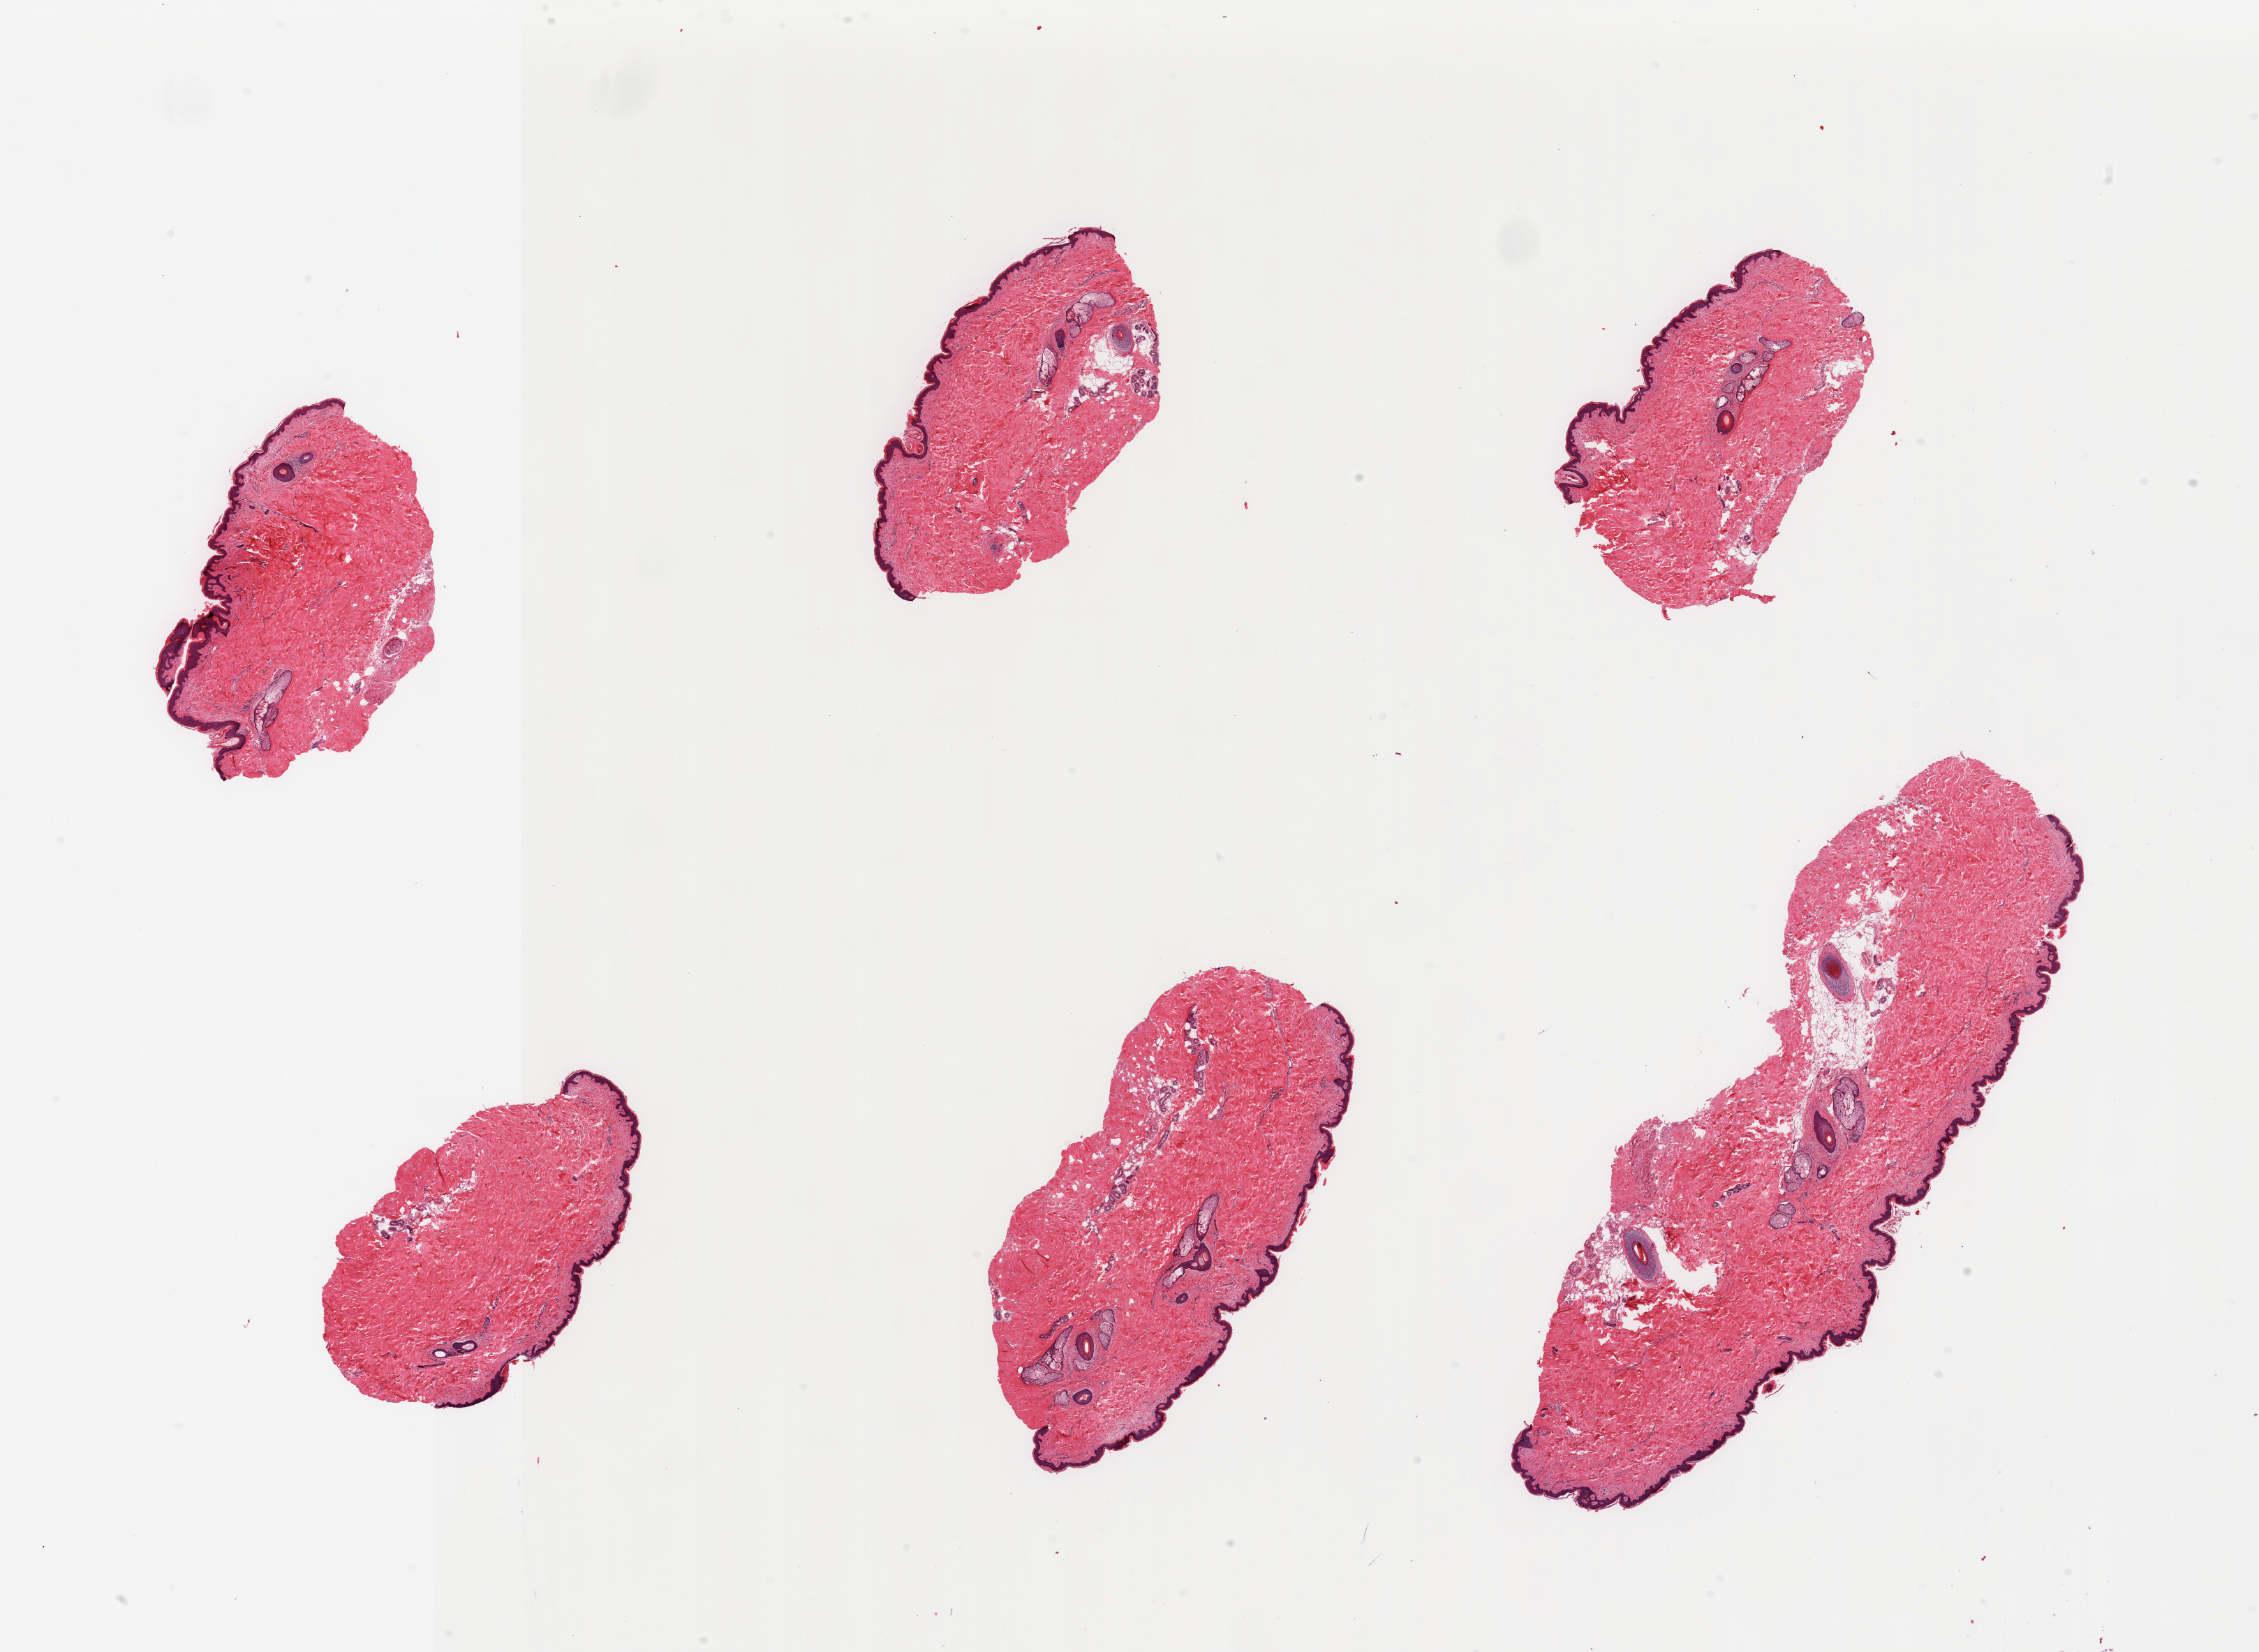
Hematoxylin and eosin (H&E) whole-slide image, brightfield, shown as a low-resolution overview of the whole scanned area (about 25.6 x 18.7 mm); PAXgene-fixed paraffin-embedded (PFPE) section; sampled site (target tissue): skin of suprapubic region; donor tissue sample. Male donor.
• review note (as recorded): 6 pieces, no significant dermal fat, squamous epithelium is ~50 microns